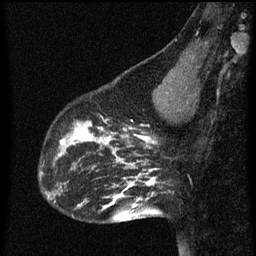
Breast MRI (dynamic contrast-enhanced), one sagittal slice; slice 20 of 60 in the series (ordered by position); dynamic contrast-enhanced series, image 2 of 3 at this slice position (ordered by acquisition); 1.5 T; TE 4.2 ms, TR 8 ms; 2 mm slice thickness; 256 × 256 image matrix, field of view 180 × 180 mm. Female patient, age 43 years.
Outlined on this slice (semi-automatic segmentation, software-assisted and operator-edited):
- analysis volume of interest (the breast-tissue region the enhancement analysis was run in; not a lesion): bounding box (x1, y1, x2, y2) in pixels: (53, 104, 101, 155)
- tumour enhancement mask (voxels above the 70 % enhancement threshold inside the analysis volume of interest): (59, 120, 101, 155)